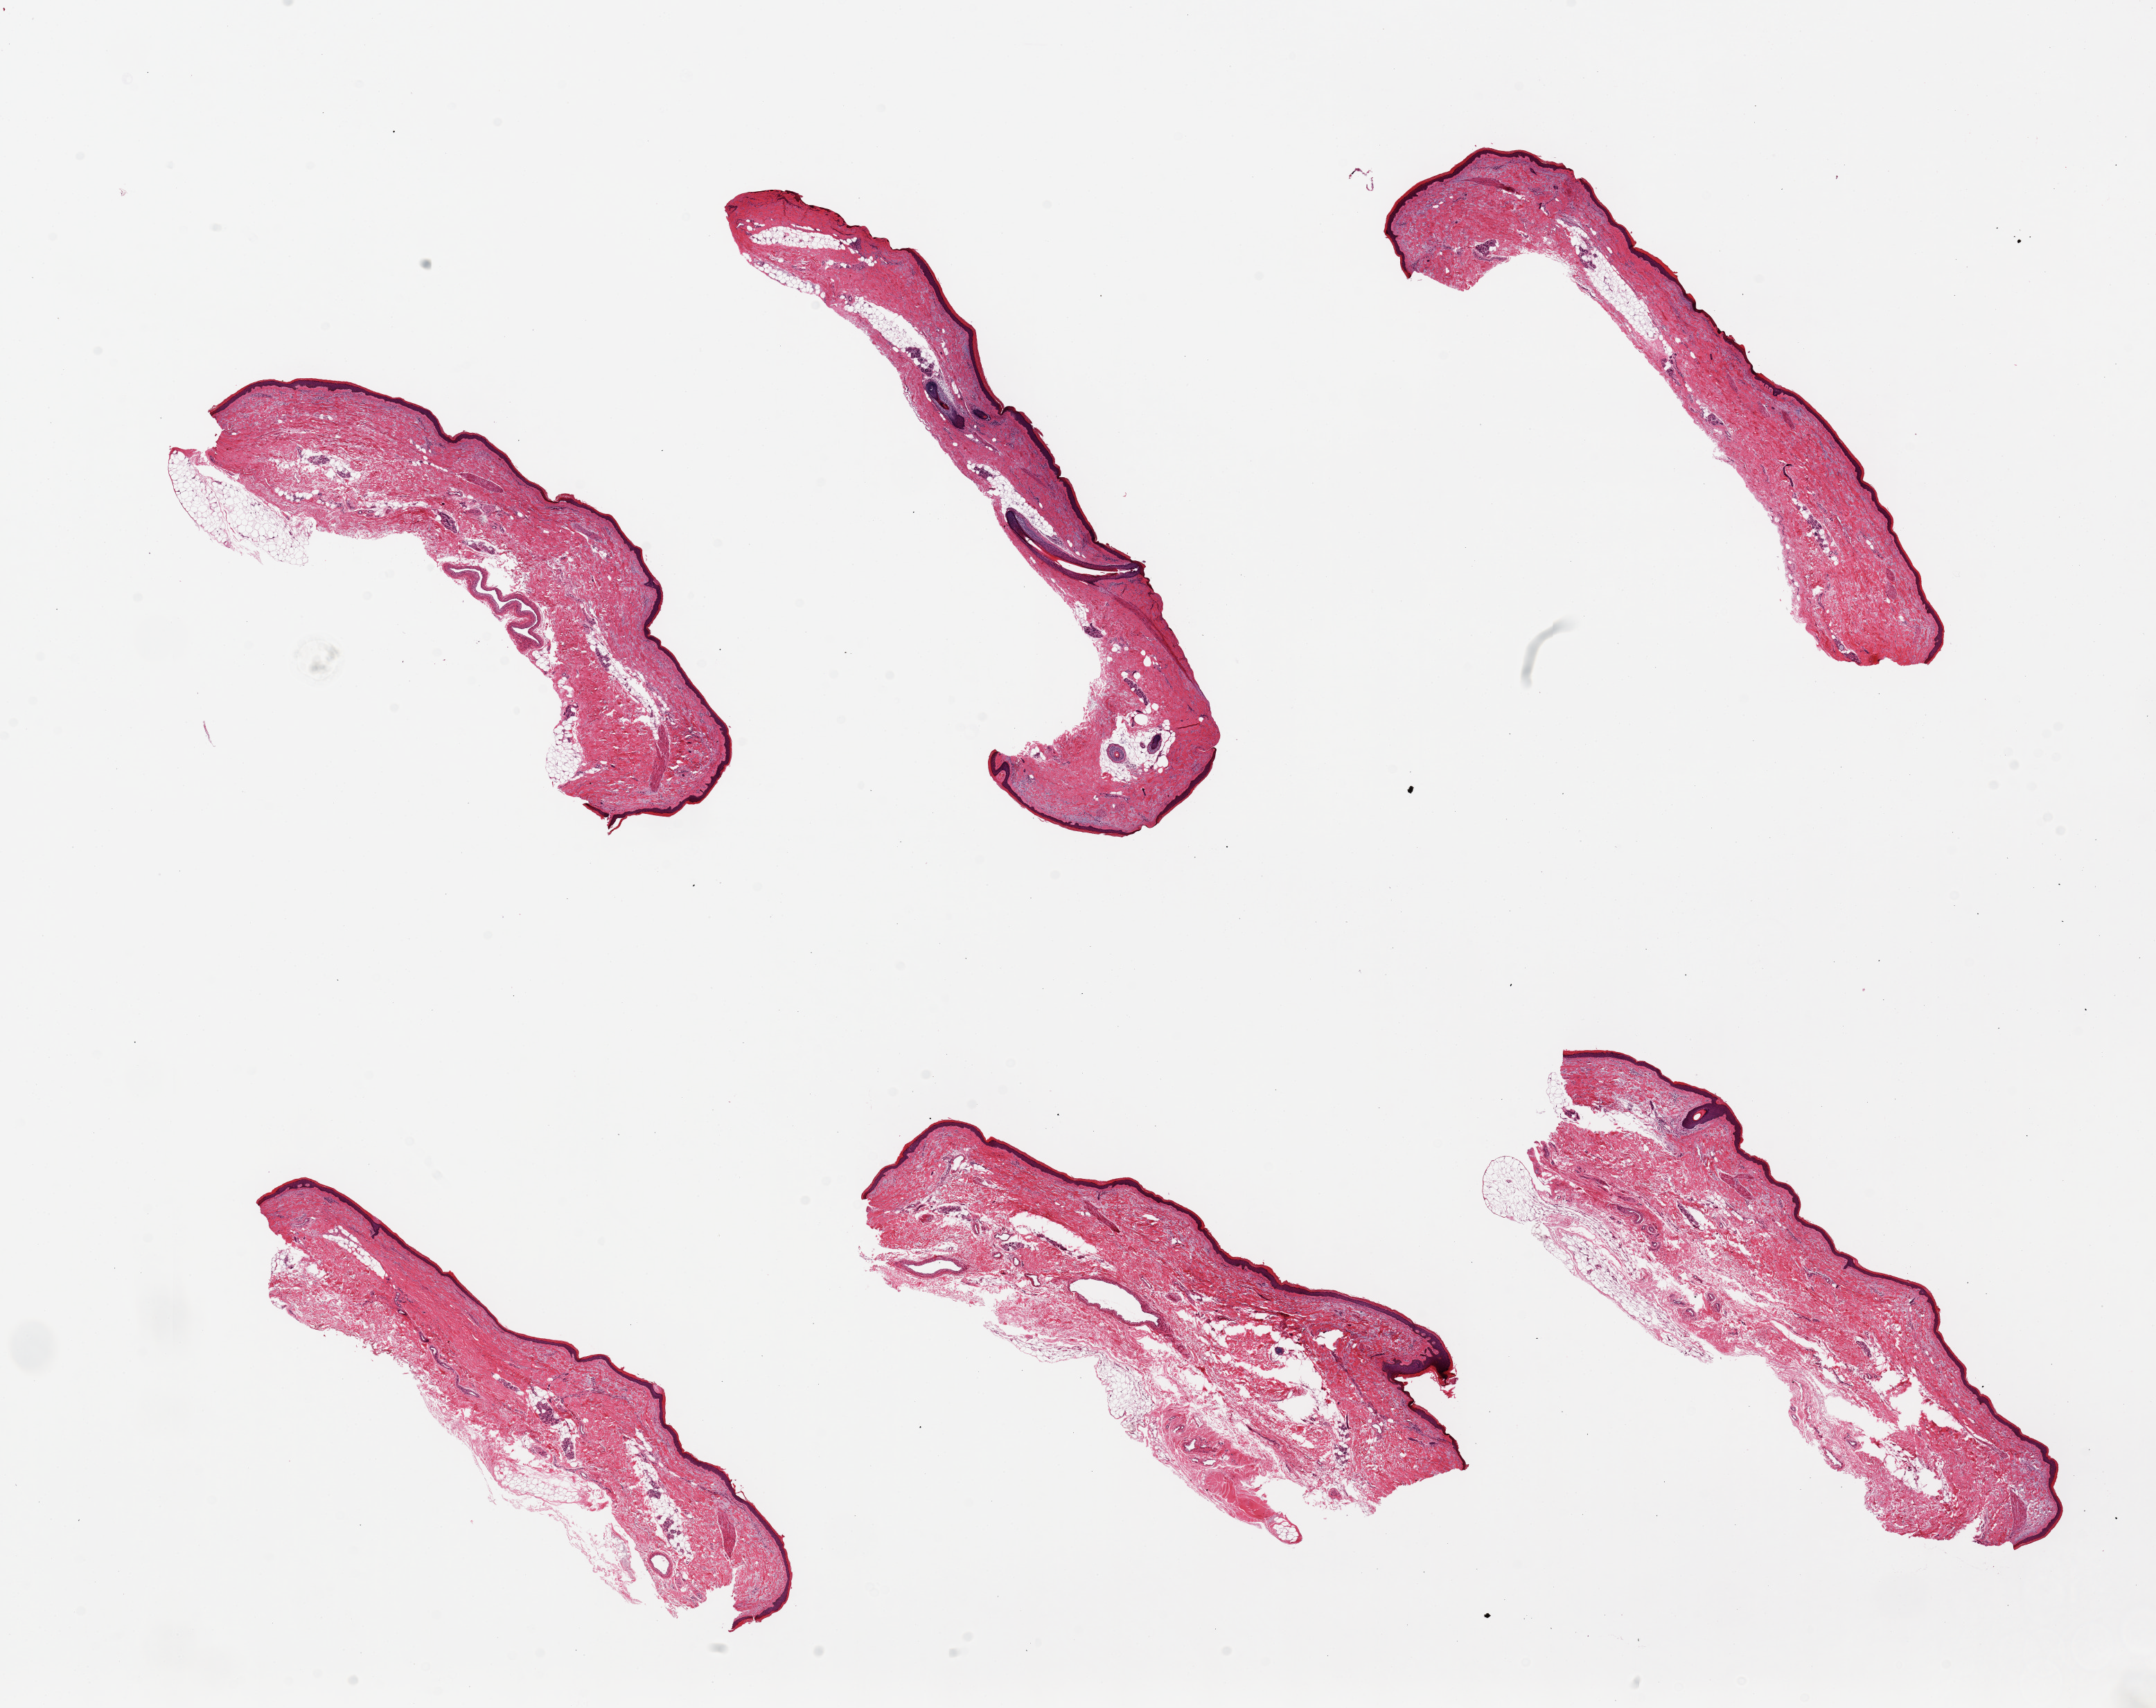
Digitized haematoxylin and eosin-stained section, whole scanned area (about 24.6 x 19.5 mm, from a 20x scan) shown as a low-resolution overview; PAXgene-fixed, paraffin-embedded tissue; target tissue: skin of lower leg; donor tissue sample. Female donor.
Pathologist's review note for this sample: 1 piece, 11x2mm; squamous epithelium is 1-1.%% thickness.